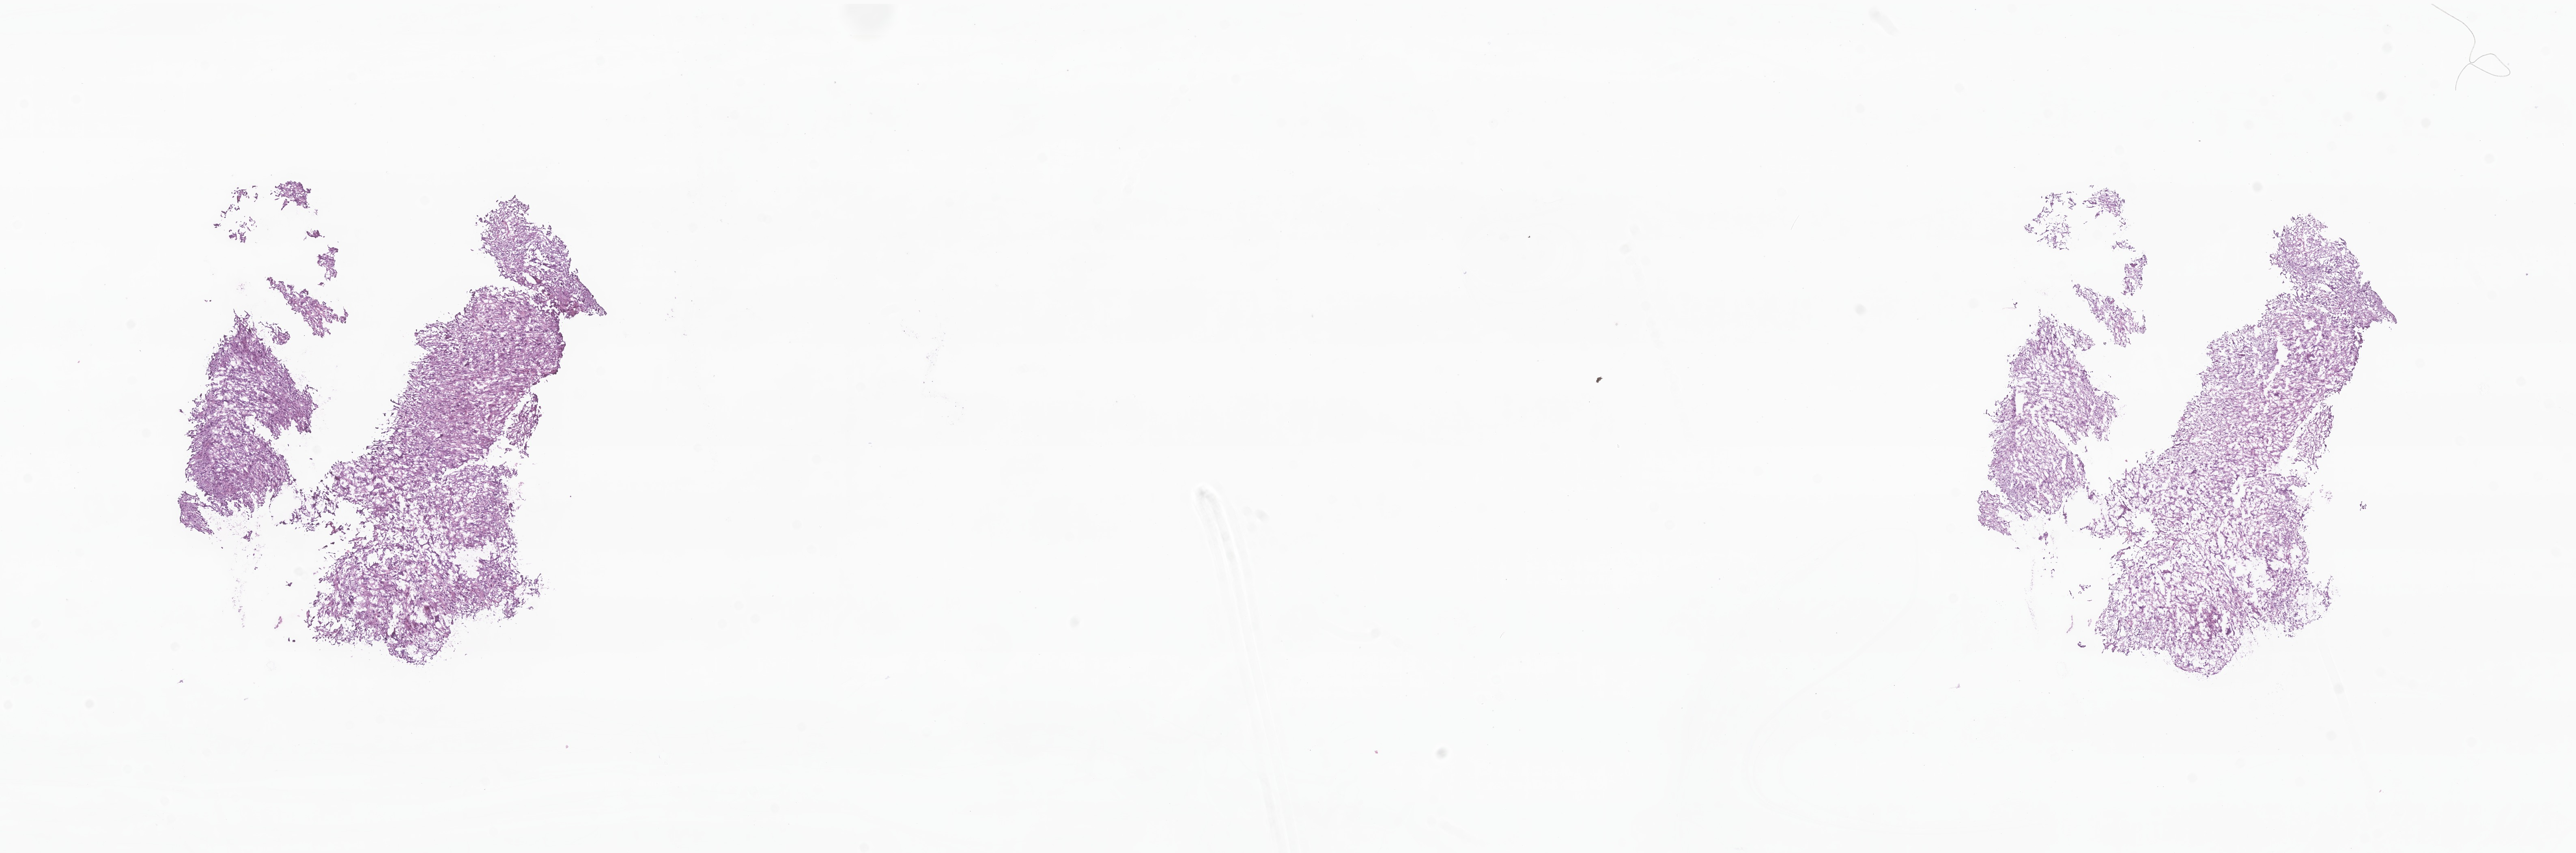
Whole-slide image, H&E stain of tumor tissue from the soft tissue of trunk, low-resolution overview of the scanned area, about 26.8 x 8.9 mm. Frozen section. Patient male; age 173 months (14 years 5 months).
Diagnosis: Undifferentiated sarcoma.